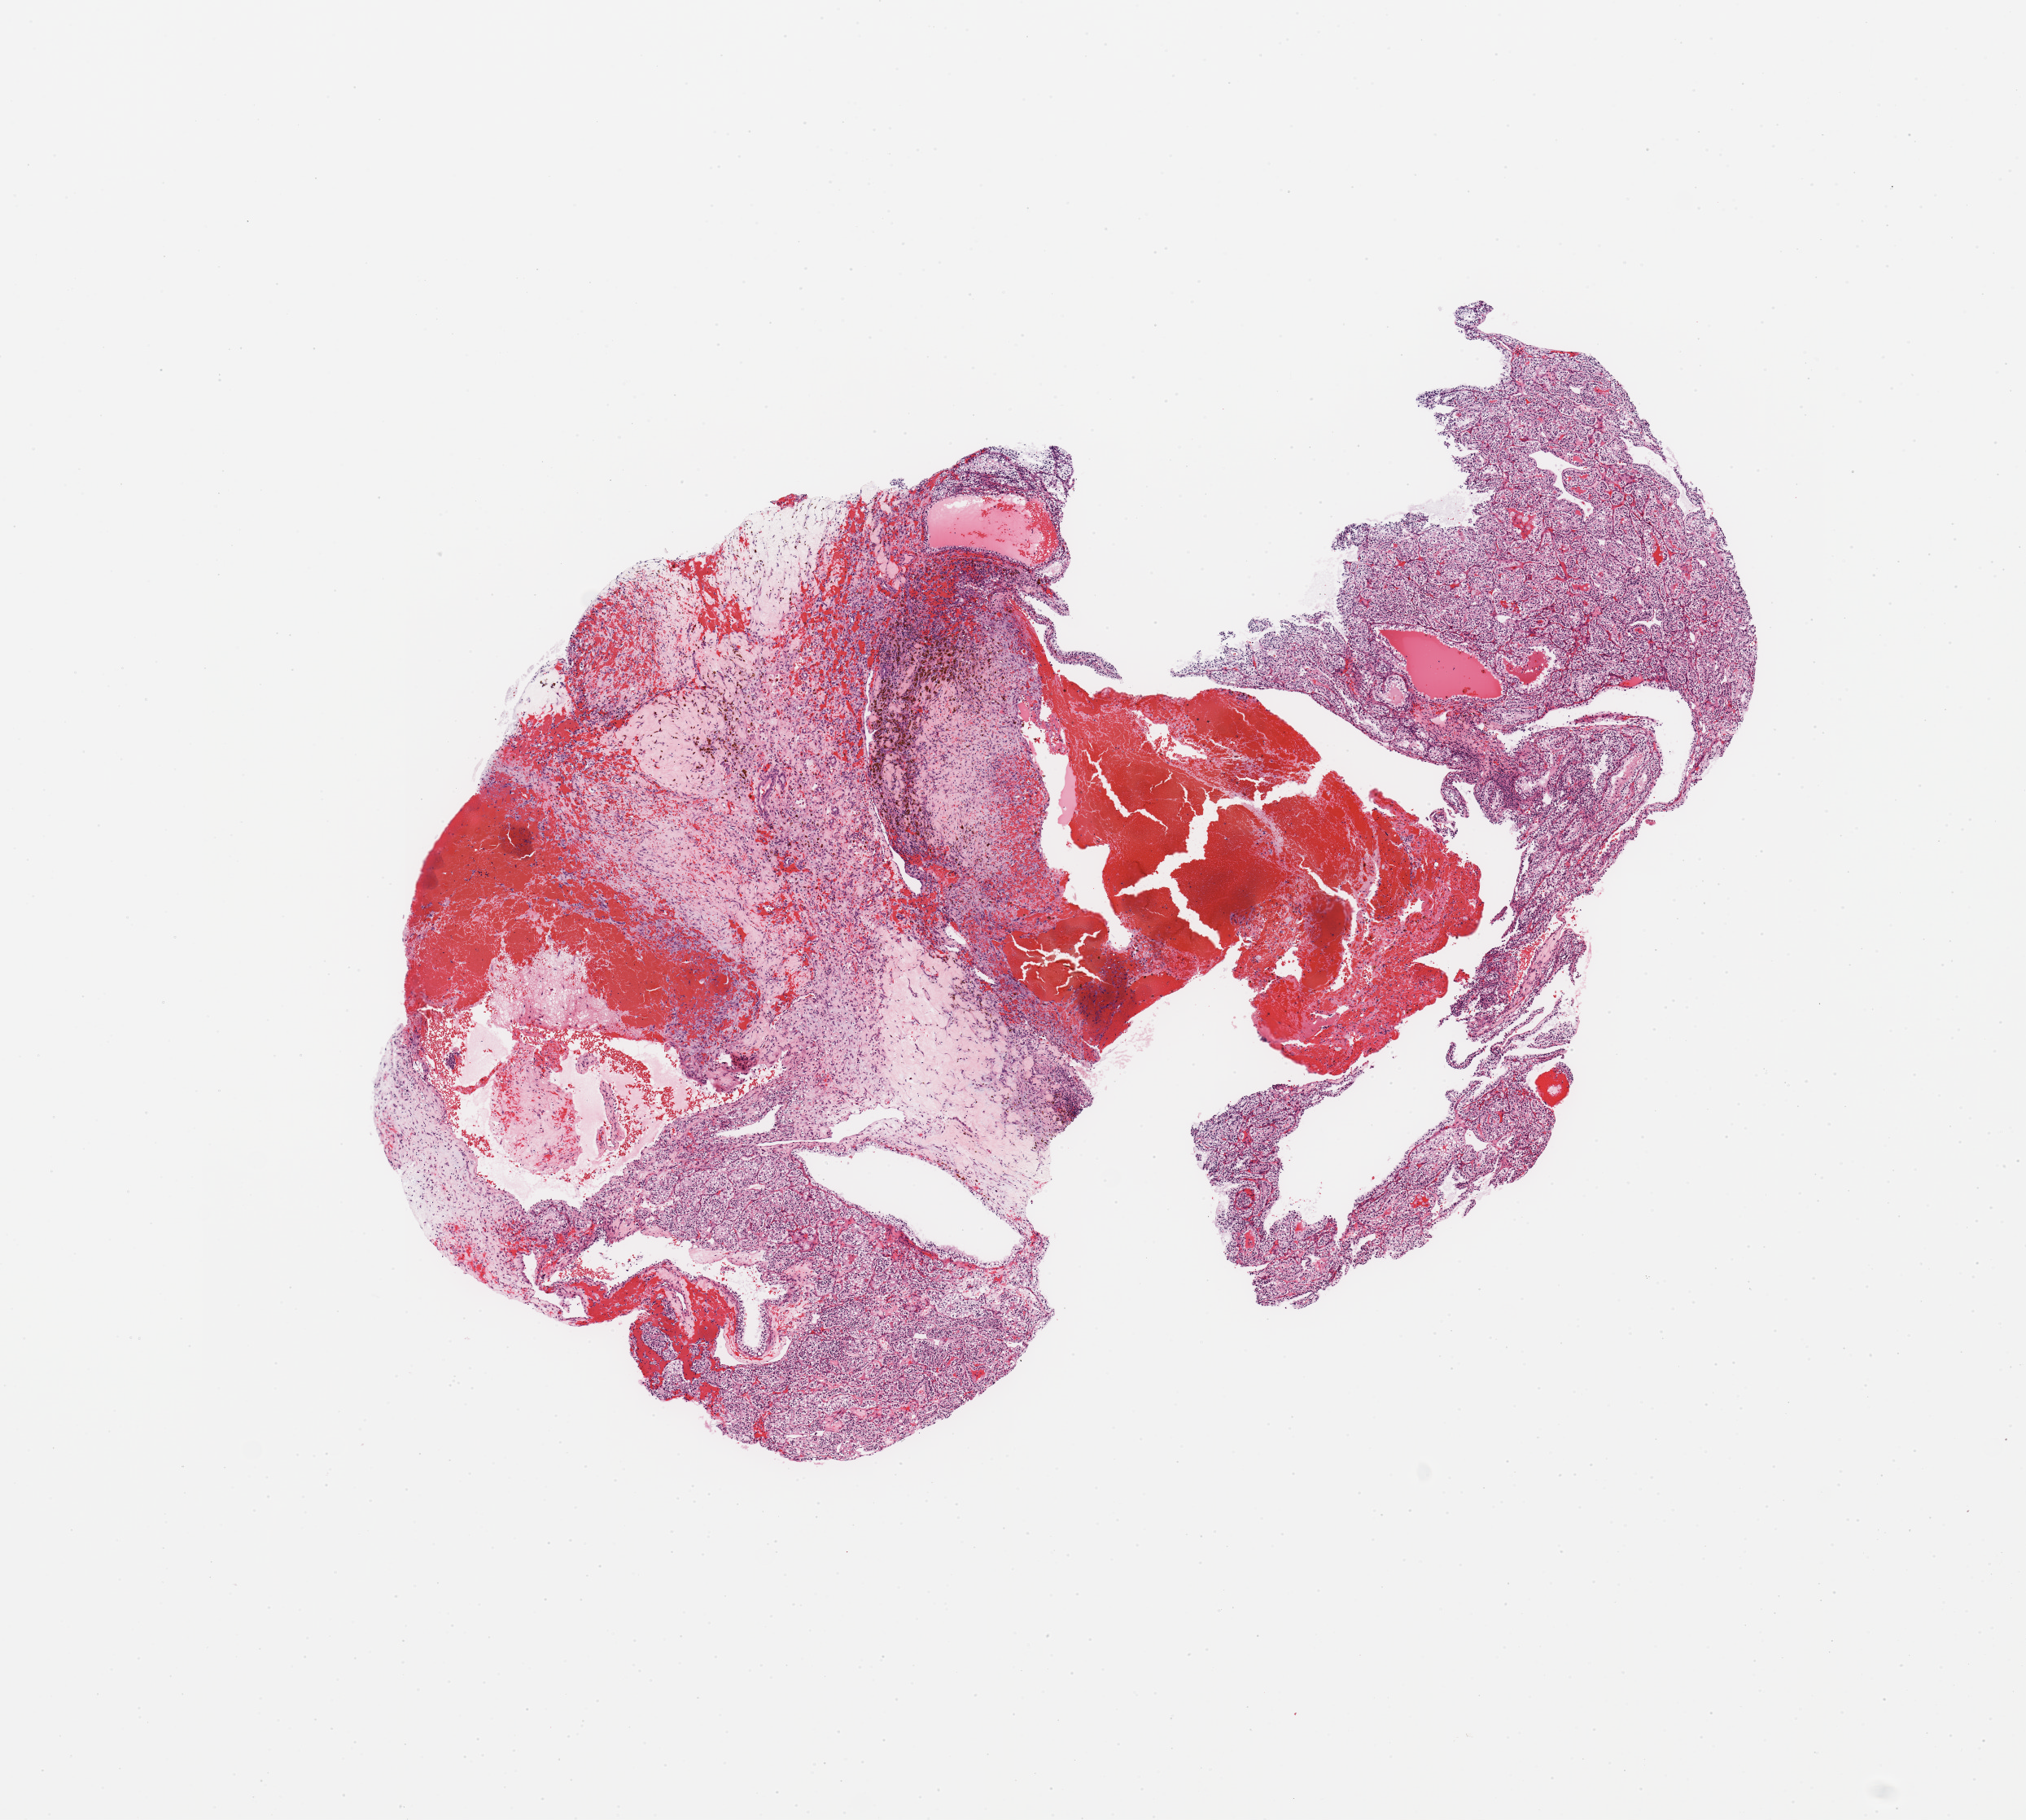
Whole-slide histology image, H&E — a low-resolution overview of the entire scanned area, about 9.8 x 8.8 mm (acquisition: 20x scan); tumour tissue sample, sampled site: kidney. Patient: male, age 35 years. Histologic grade: G3 (poorly differentiated). Pathologist review of this section (percent, as recorded): tumour nuclei 80%, necrosis 10%.
AJCC pathologic stage: I. Primary tumour site (as recorded): upper pole. Diagnosis: Renal cell carcinoma, NOS.